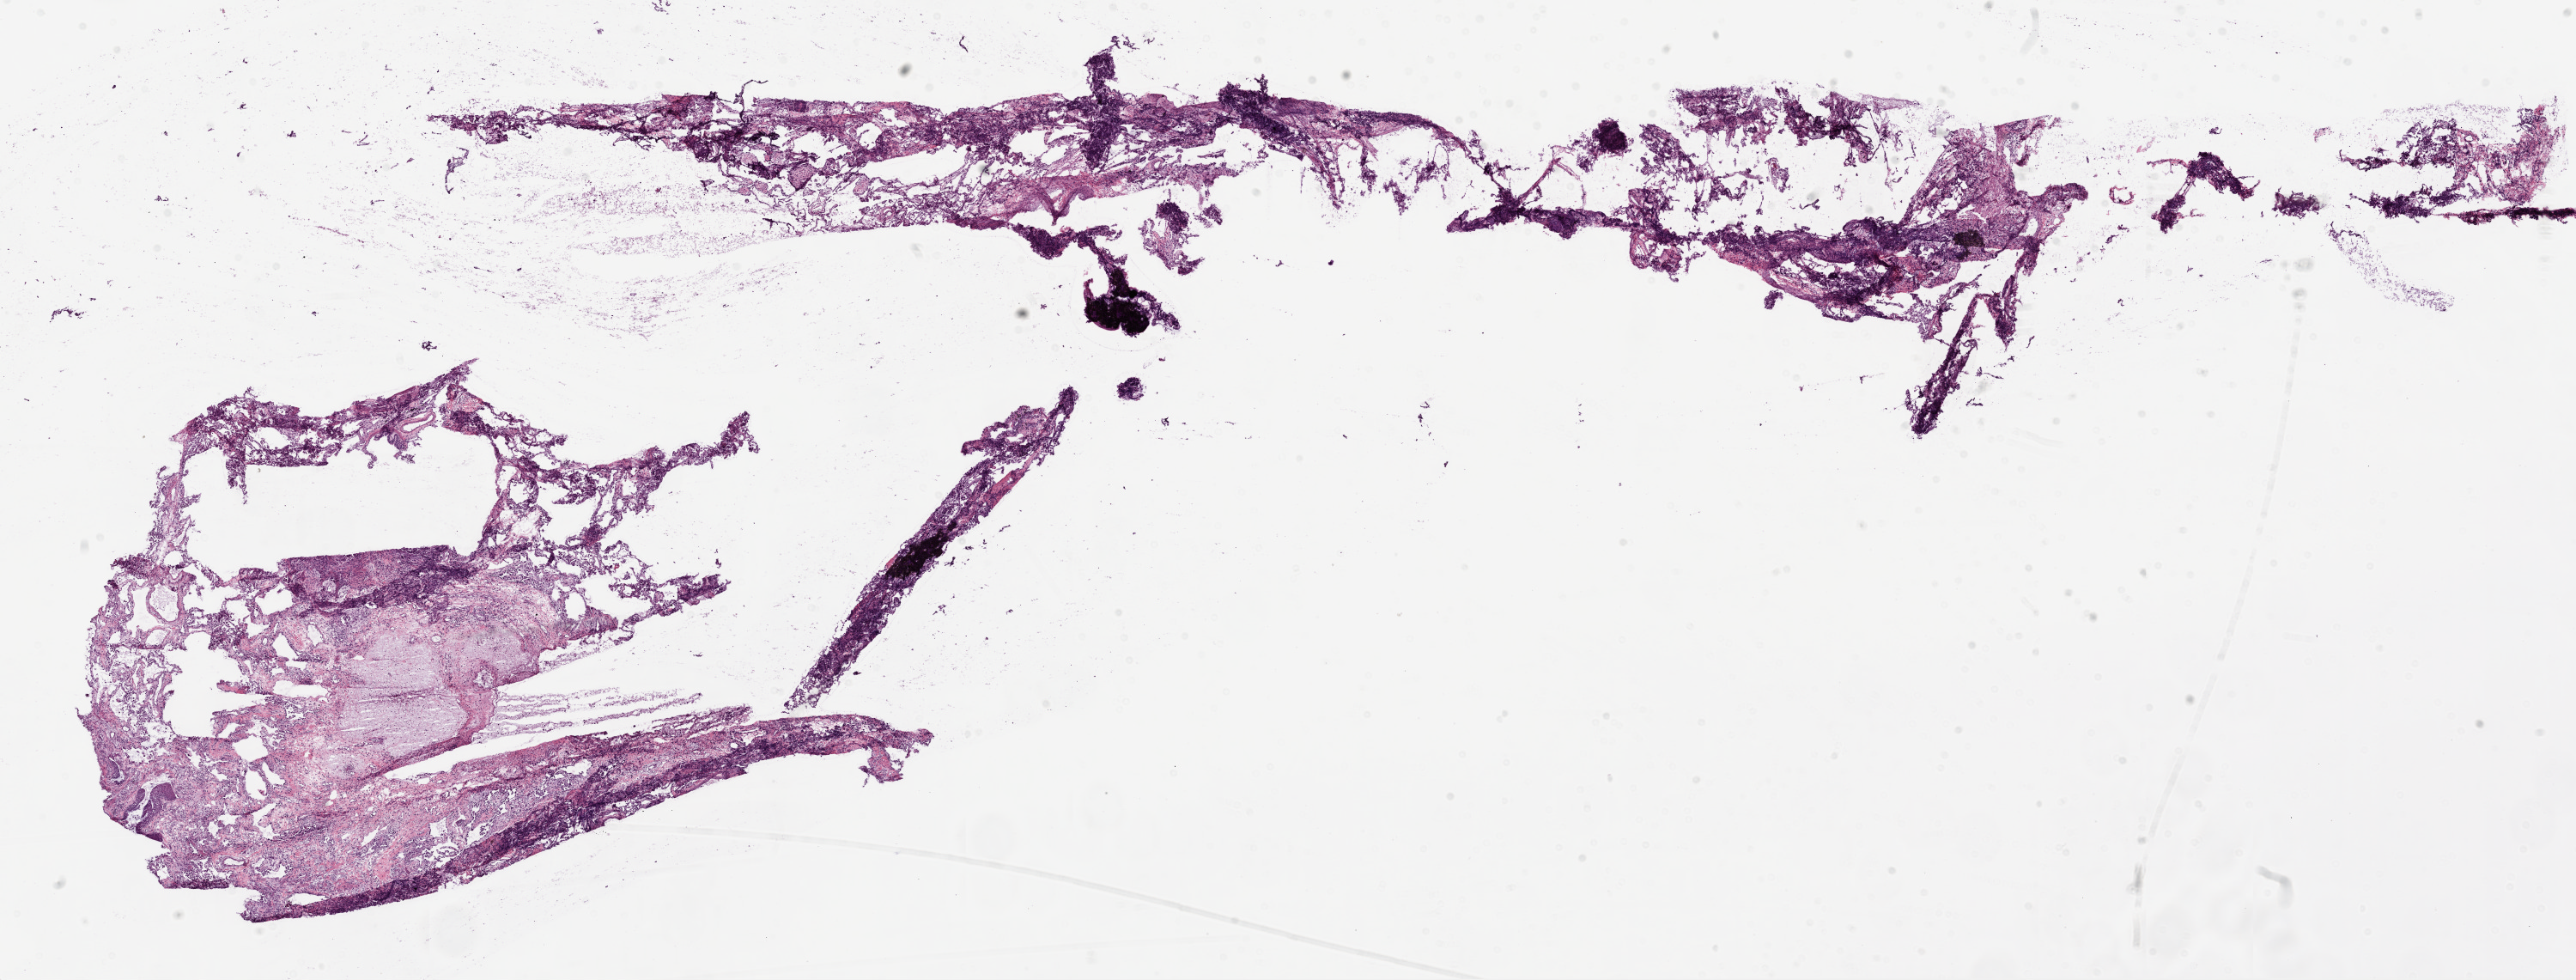
Digitized H&E tissue section (whole slide) — whole scanned area (about 24.1 x 9.2 mm) shown as a low-resolution overview. Frozen section from the top of the tissue portion. Lung, solid tissue normal (non-tumour tissue) sample. Male, age 70 years at initial diagnosis.
* this section: solid tissue normal (non-tumour) sample from the same patient
* patient diagnosis: Squamous cell carcinoma, NOS (upper lobe, lung)